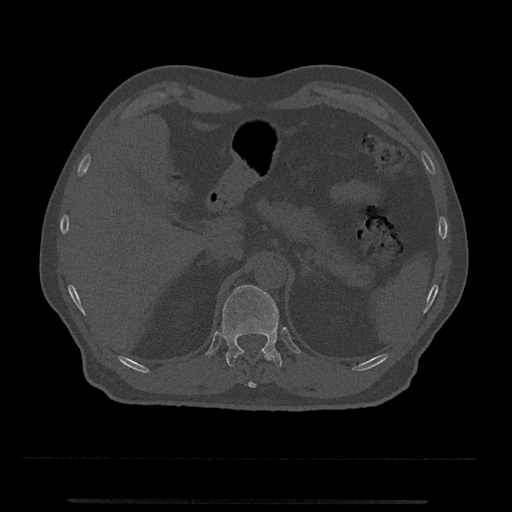
CT including the spine, one axial slice; slice 422 of 797 in the series (ordered by position); 120 kVp; bone window (W 1800 / L 400 HU); 512 × 512 image matrix. Patient: male, 63 years. Case-level facts recorded for this patient, not image findings: primary cancer: prostate.
Structures marked on this image (semi-automatically segmented with operator editing):
- T11 vertebra: bounding box <236,350,272,388> (left, top, right, bottom; pixels)
- T12 vertebra: <222,285,282,367>